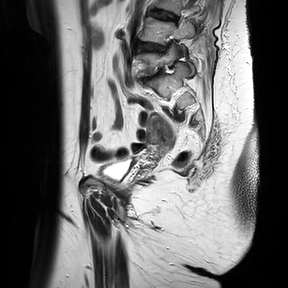
Pelvic MRI for cervical cancer, one sagittal slice. Slice 25 of 37 in the series (ordered by position). T2-weighted. 1.5 T. TE 100 ms, TR 4174.1 ms. 4 mm slice thickness. 288 × 288 image matrix, field of view 300 × 300 mm. Female patient, age 65 years.
Outlined on this slice (outlined manually by an expert reader):
- uterus and cervix: bounding box (x1, y1, x2, y2) in pixels: (148, 114, 174, 148)